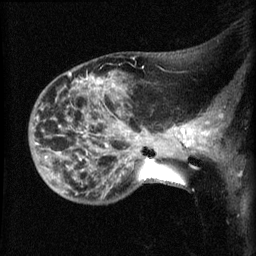
Breast MRI (dynamic contrast-enhanced), one sagittal slice. Position 20 of 60 along the scan axis. Dynamic contrast-enhanced series, image 2 of 3 at this slice position (ordered by acquisition). 1.5 T. TE 4.2 ms, TR 8.2 ms. 256 × 256 image matrix. Female patient, age 50 years.
Outlined on this slice (semi-automatic segmentation, software-assisted and operator-edited):
- analysis volume of interest (the breast-tissue region the enhancement analysis was run in; not a lesion): box from (x=38, y=76) to (x=169, y=204) px
- tumour enhancement mask (voxels above the 70 % enhancement threshold inside the analysis volume of interest): (x=85, y=77)–(x=165, y=136)